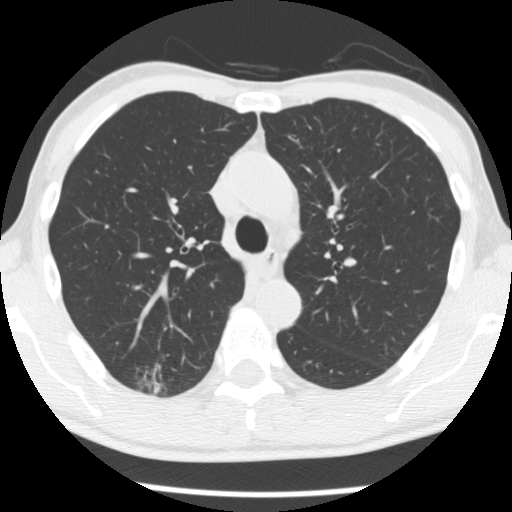
Chest CT (low-dose screening protocol), one axial image; first (baseline) screen; lung window (W 1500 / L -600 HU); 2.5 mm slice thickness; 120 kVp; slice 87 of 277 in the series; 512 × 512 image matrix, field of view 320 × 320 mm. Male, age 66 years at enrolment. Former smoker at enrolment.
Lesion marked by an expert reader, box from (x=130, y=356) to (x=190, y=404) px. The screening reader recorded 4 non-calcified nodules or masses ≥4 mm on this exam (right upper lobe, right upper lobe, right upper lobe, left lower lobe); which of them this box marks is not recorded. Official screen result: positive, change unspecified: nodule(s) >= 4 mm or enlarging nodule(s), mass(es), or other non-specific abnormalities suspicious for lung cancer. Participant outcome: lung cancer diagnosed 503 days after this screen (after the second annual screen) — adenocarcinoma, NOS, right upper lobe, undifferentiated (G4), stage IA (AJCC 6th edition), 20 mm at pathology.